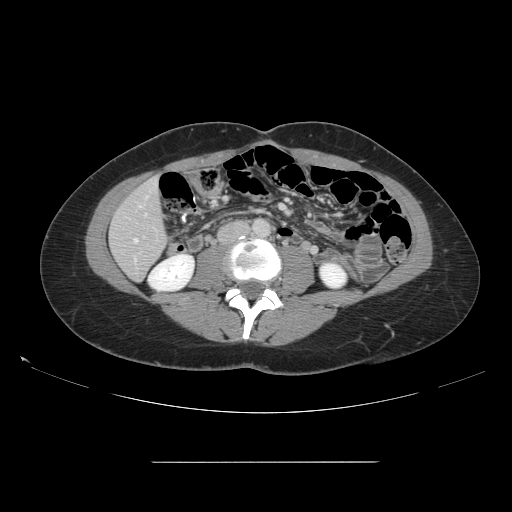
Contrast-enhanced abdominal CT, one axial slice. Position 35 of 151 along the scan axis. Intravenous contrast given. Soft-tissue window (W 400 / L 40 HU). 2.5 mm slice thickness. 512 × 512 image matrix. Female patient, age 46 years. Case-level facts recorded for this patient, not image findings: diagnosis: colorectal cancer liver metastases, imaged before liver resection; multiple liver metastases: yes; largest metastasis: 3 cm; disease in both lobes: yes.
Outlined on this slice (manually delineated by an expert):
- hepatic veins: bounding box [x1, y1, x2, y2] px = [134, 239, 137, 242]
- liver: [111, 179, 167, 280]
- planned liver remnant (the part of the liver to remain after resection): [111, 179, 167, 280]